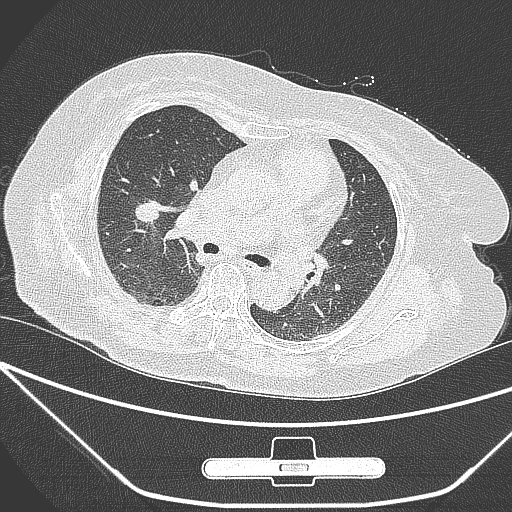
Chest CT, one axial slice. Position 158 of 245 along the scan axis. Lung window (W 1500 / L -600 HU). 512 × 512 image matrix, field of view 365 × 365 mm. Patient: female, 65 years. Case-level facts recorded for this patient, not image findings: clinical TNM (as recorded): T1c N0 M0; histopathological grade: G3.
Structures marked on this image (bounding box drawn by a radiologist):
- lung tumour (recorded histology: adenocarcinoma): bounding box [x1, y1, x2, y2] px = [133, 196, 167, 224]